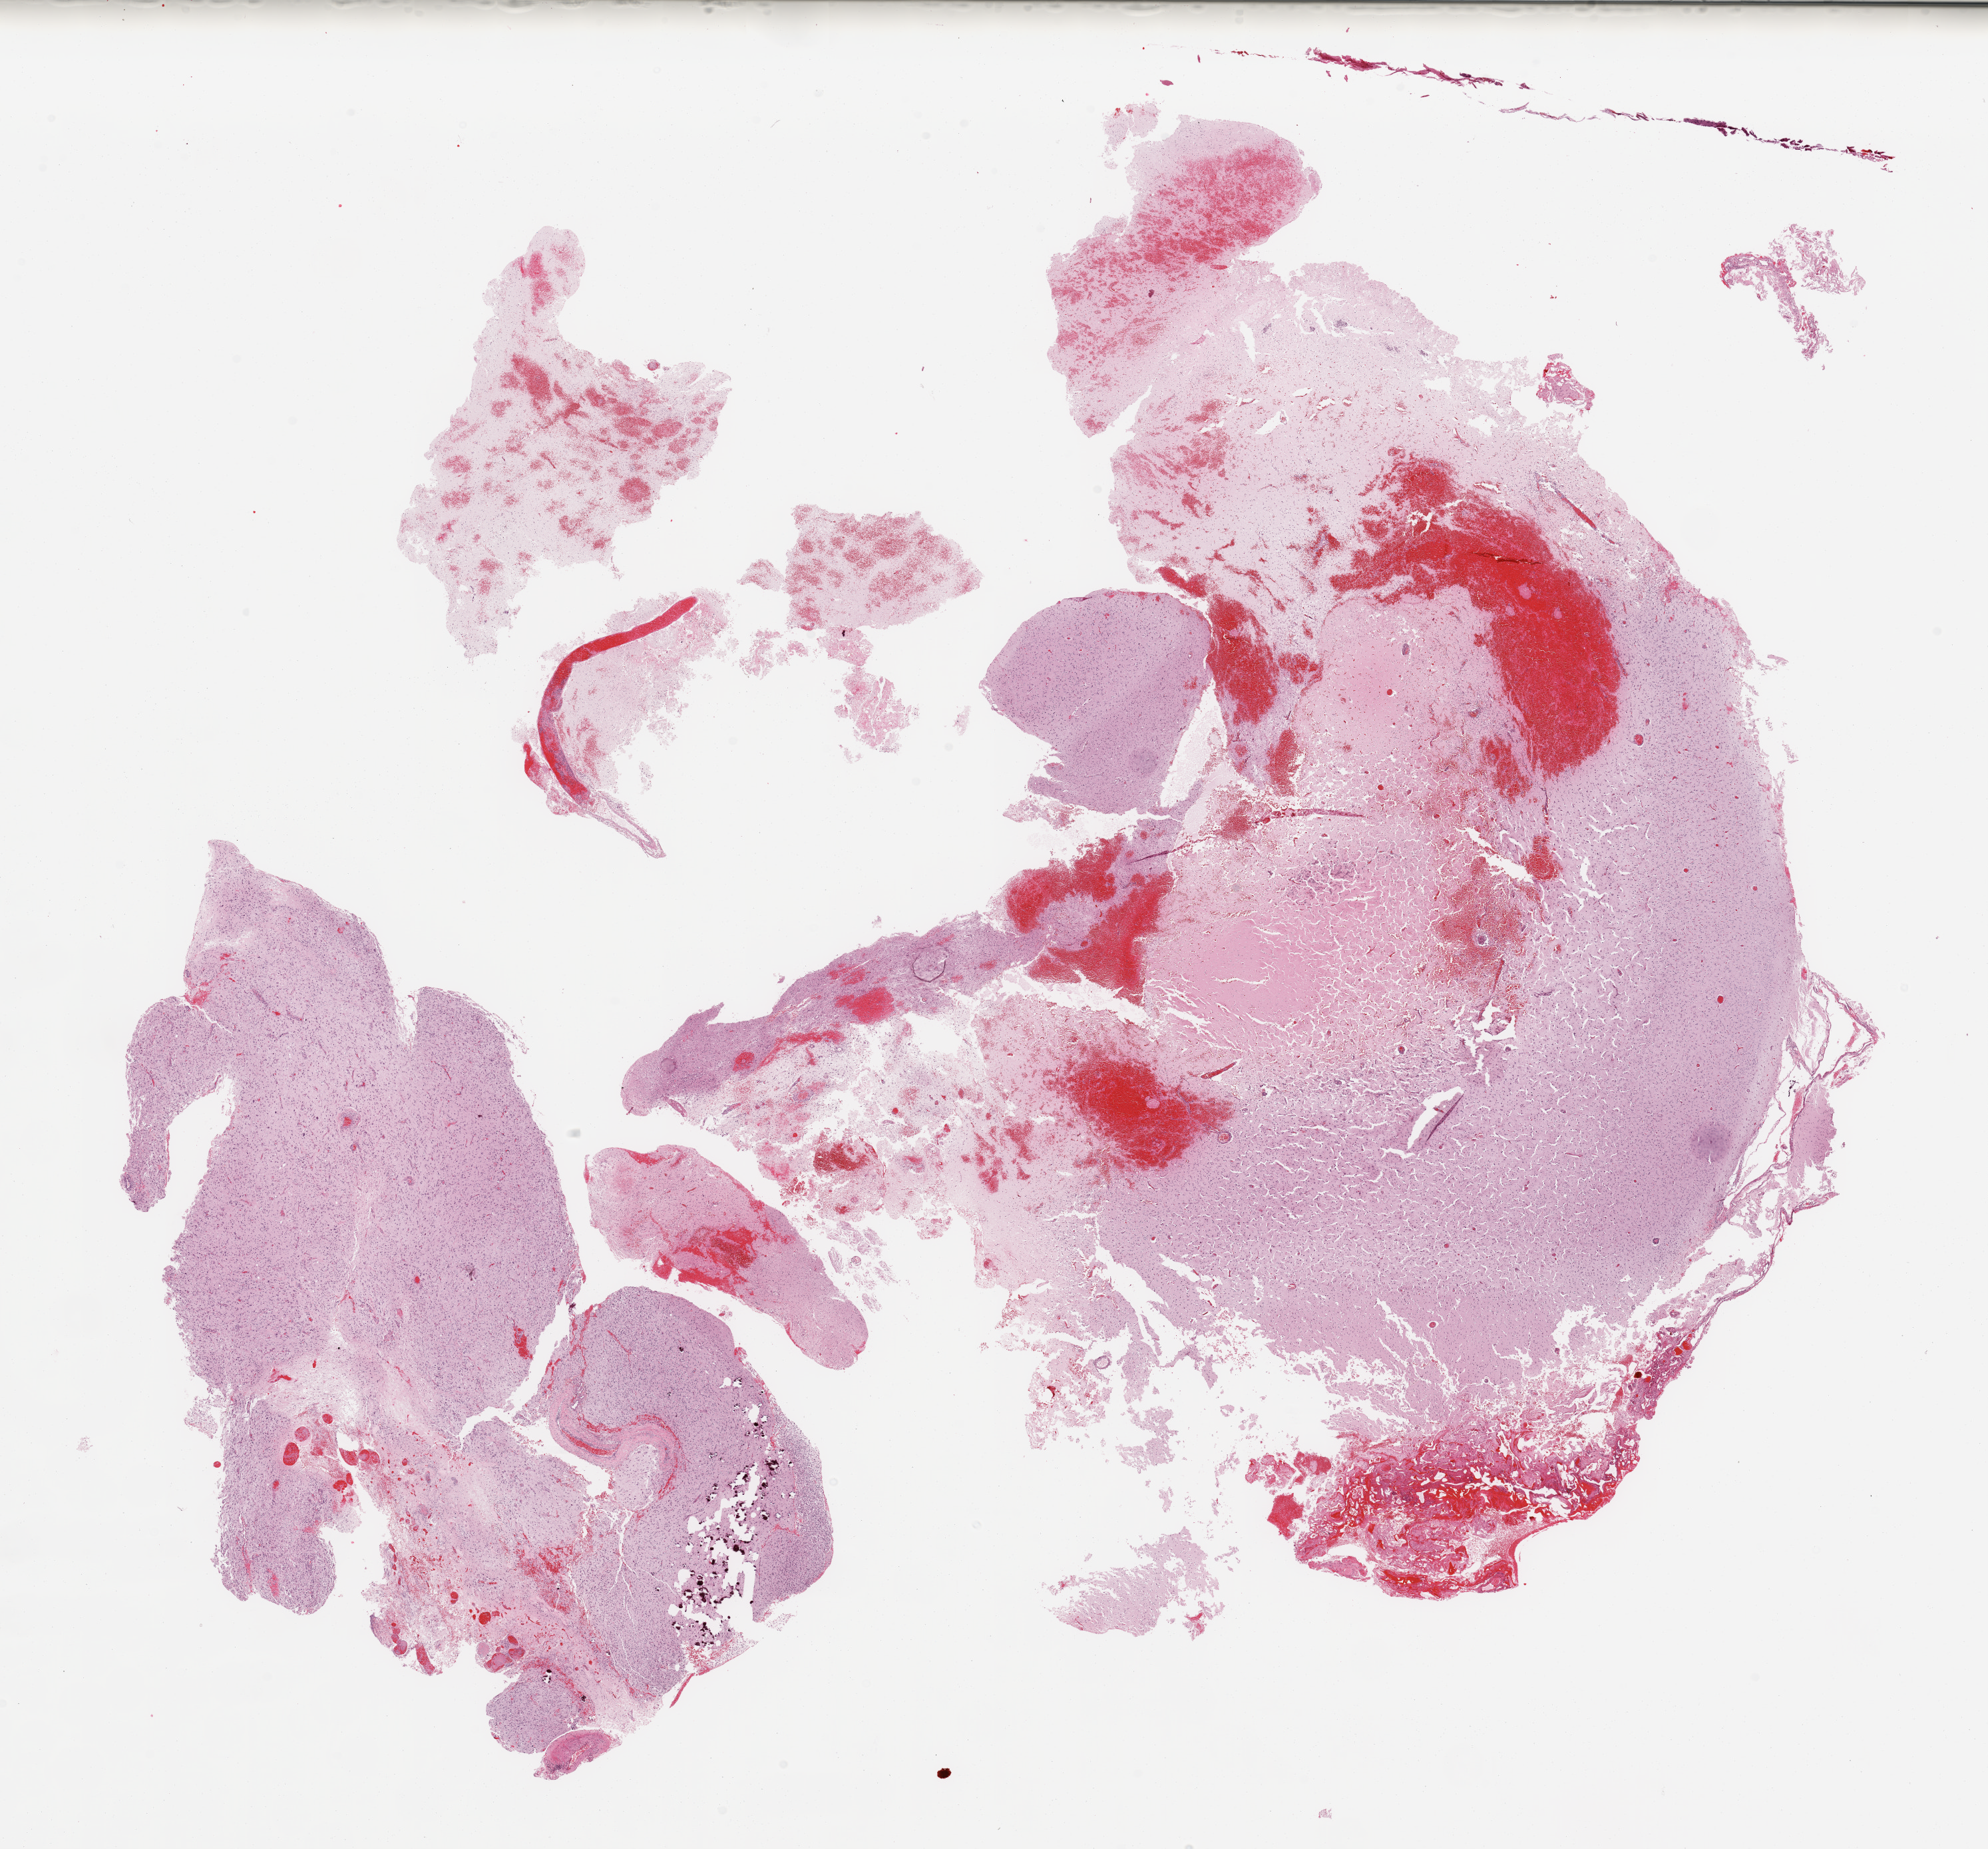
Whole-slide histology image, Hematoxylin and eosin (H&E) stained — shown as a low-resolution overview of the whole scanned area (about 23.6 x 22.0 mm, from a 20x scan). Tumour tissue sample, sampled site: occipital cortex. Male, 52 y/o. Pathologist review of this section (percent, as recorded): tumour nuclei 60%, necrosis 25%.
• diagnosis: Glioblastoma
• primary tumour site (as recorded): occipital lobe